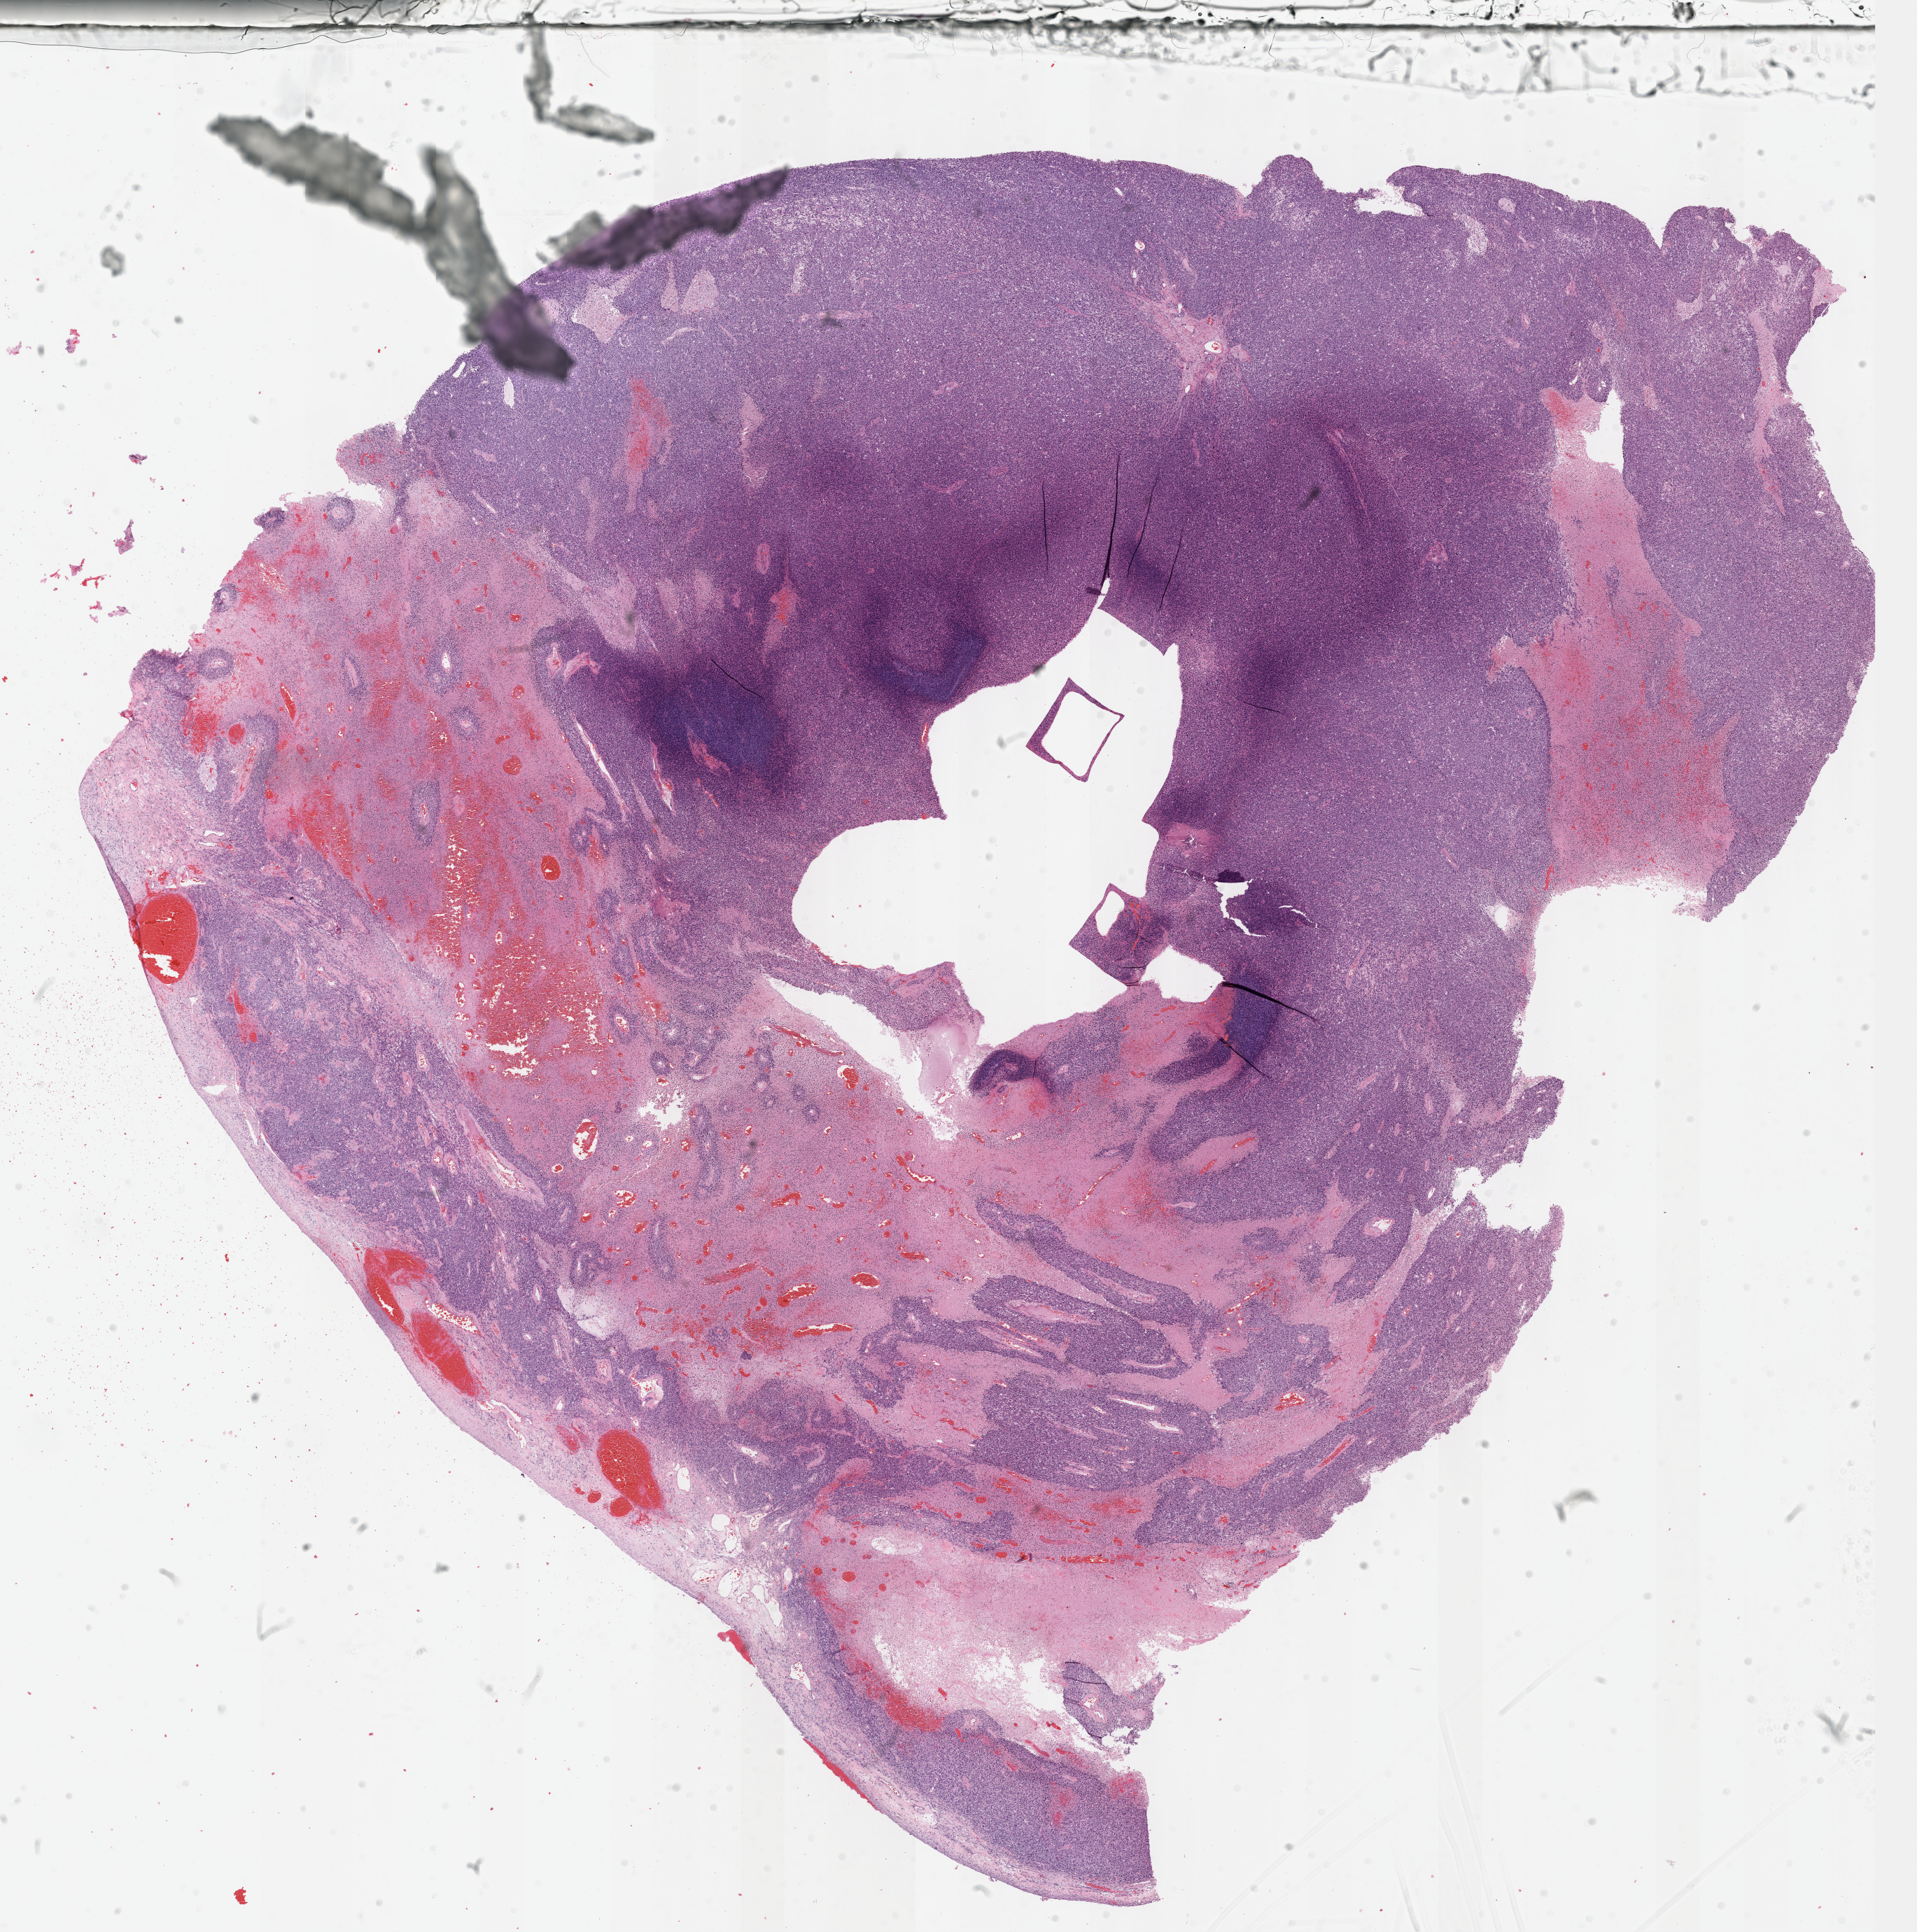
Whole-slide histology image, H&E-stained, a low-resolution overview of the entire scanned area, about 22.1 x 22.3 mm; formalin-fixed paraffin-embedded (FFPE) diagnostic section; primary tumour sample from the uterus. Female, age 58 years at initial diagnosis.
* pathologic diagnosis: Leiomyosarcoma, NOS